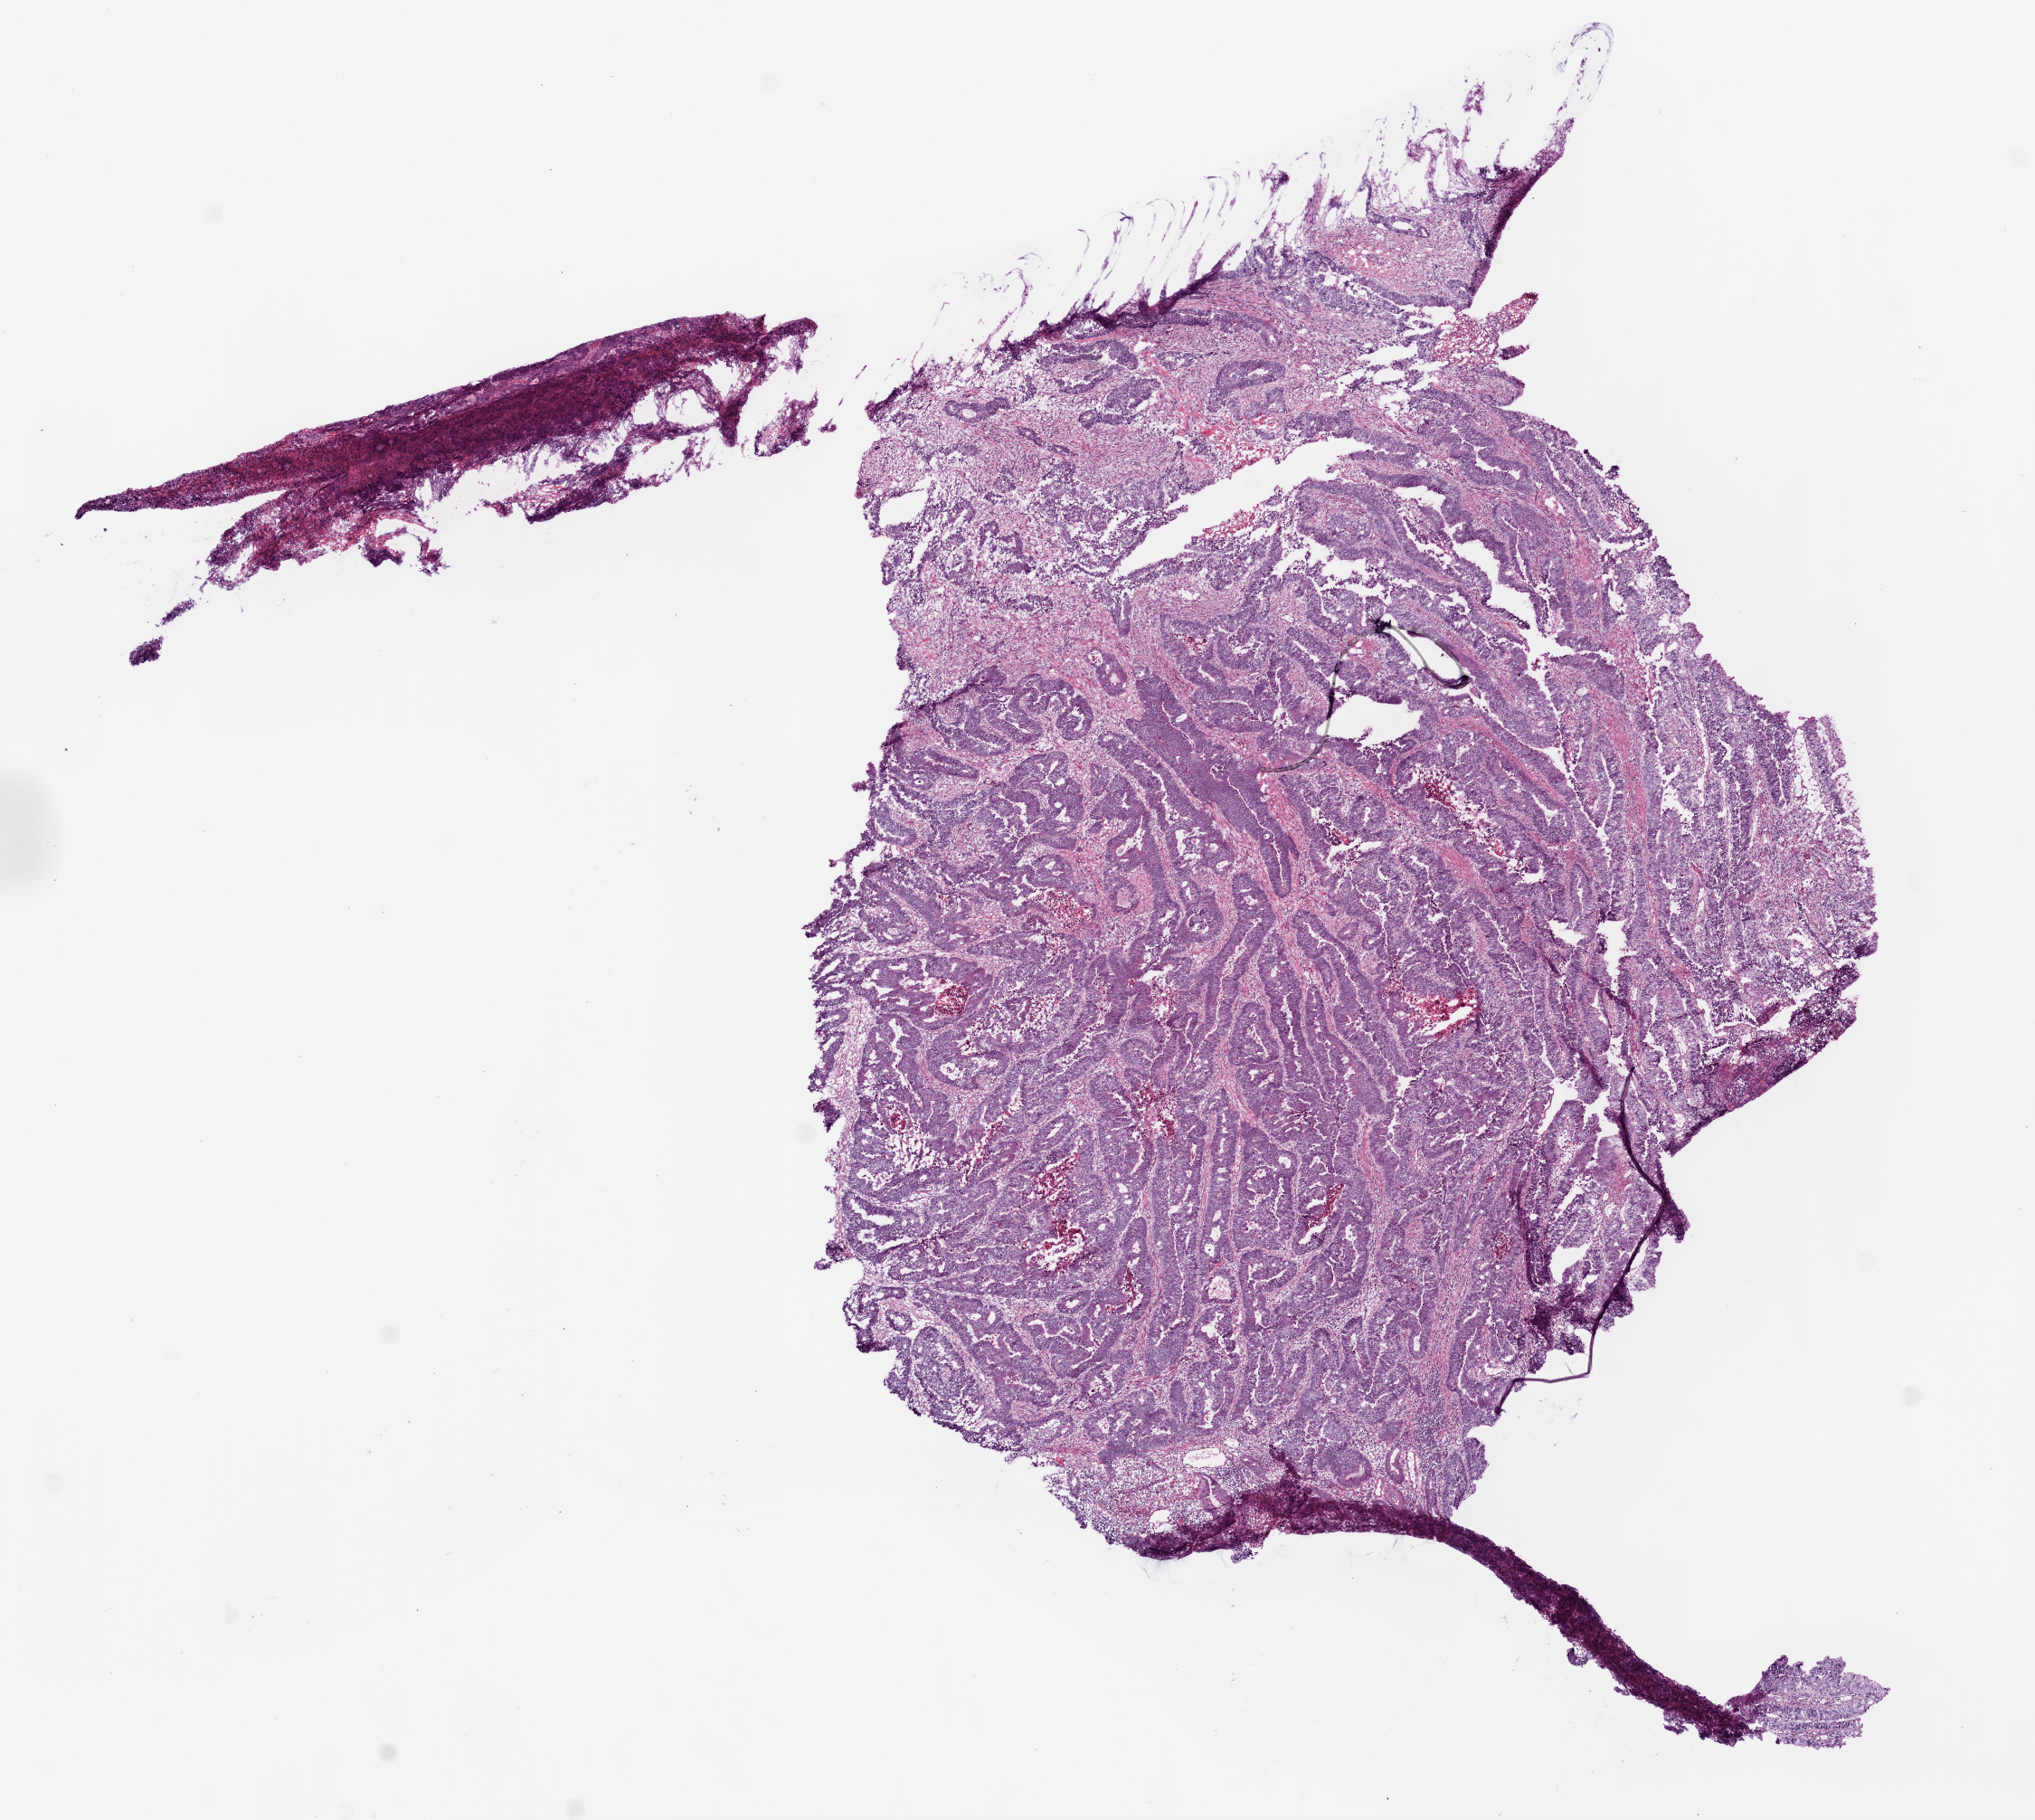
Digitized H&E tissue section (whole slide), whole scanned area (about 9.0 x 8.1 mm, from a 20x scan) shown as a low-resolution overview; frozen section from the top of the tissue portion; sample: primary tumour, rectum. Male, age 75 years at initial diagnosis. Composition of this section per pathologist review: tumour cells 81%, tumour nuclei 75%, normal cells 1%, stromal cells 10%, necrosis 8%.
• TNM: T3 N1 M1
• AJCC pathologic stage: IV (6th edition)
• pathologic diagnosis: Adenocarcinoma, NOS (colon, NOS)
• lymph nodes positive (case pathology): 1 of 28 examined